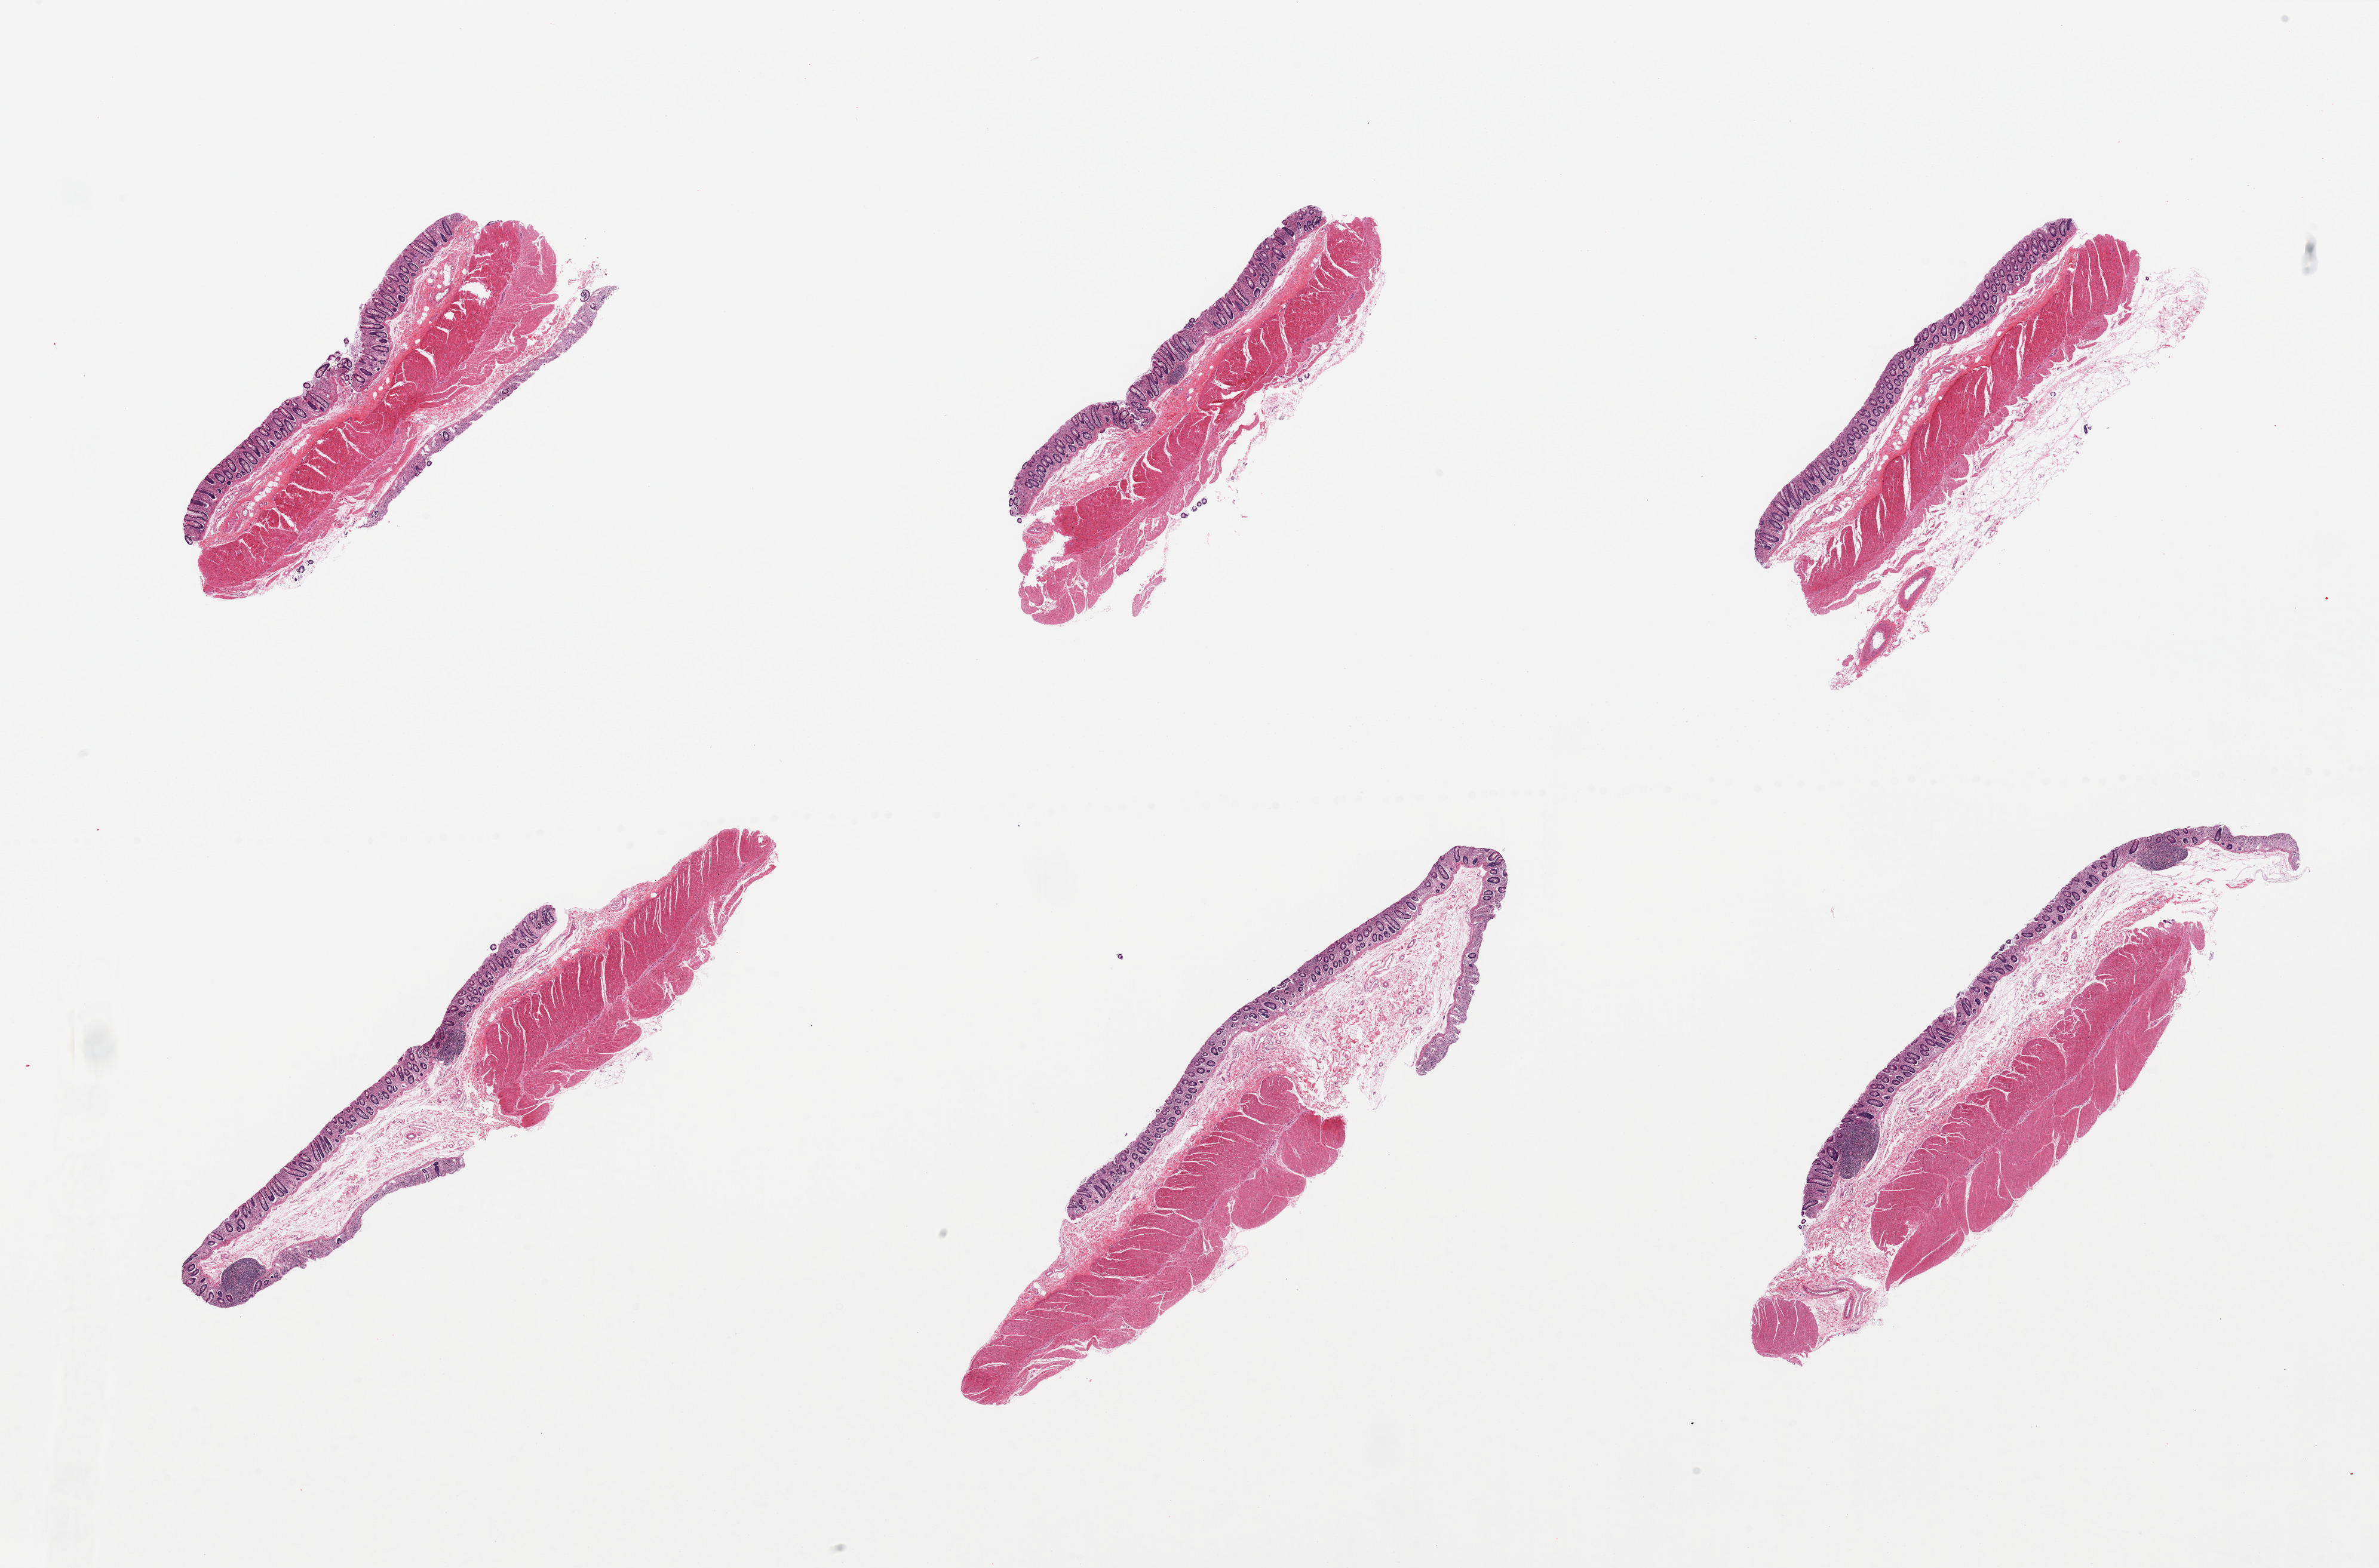
Digitized H&E-stained section, whole scanned area (about 31.5 x 20.8 mm, slide scanned at 20x) shown as a low-resolution overview; PAXgene-fixed paraffin-embedded (PFPE) section; sampled site (target tissue): transverse colon; tissue donor sample. Donor sex: female.
* review note (as recorded): 6 pieces